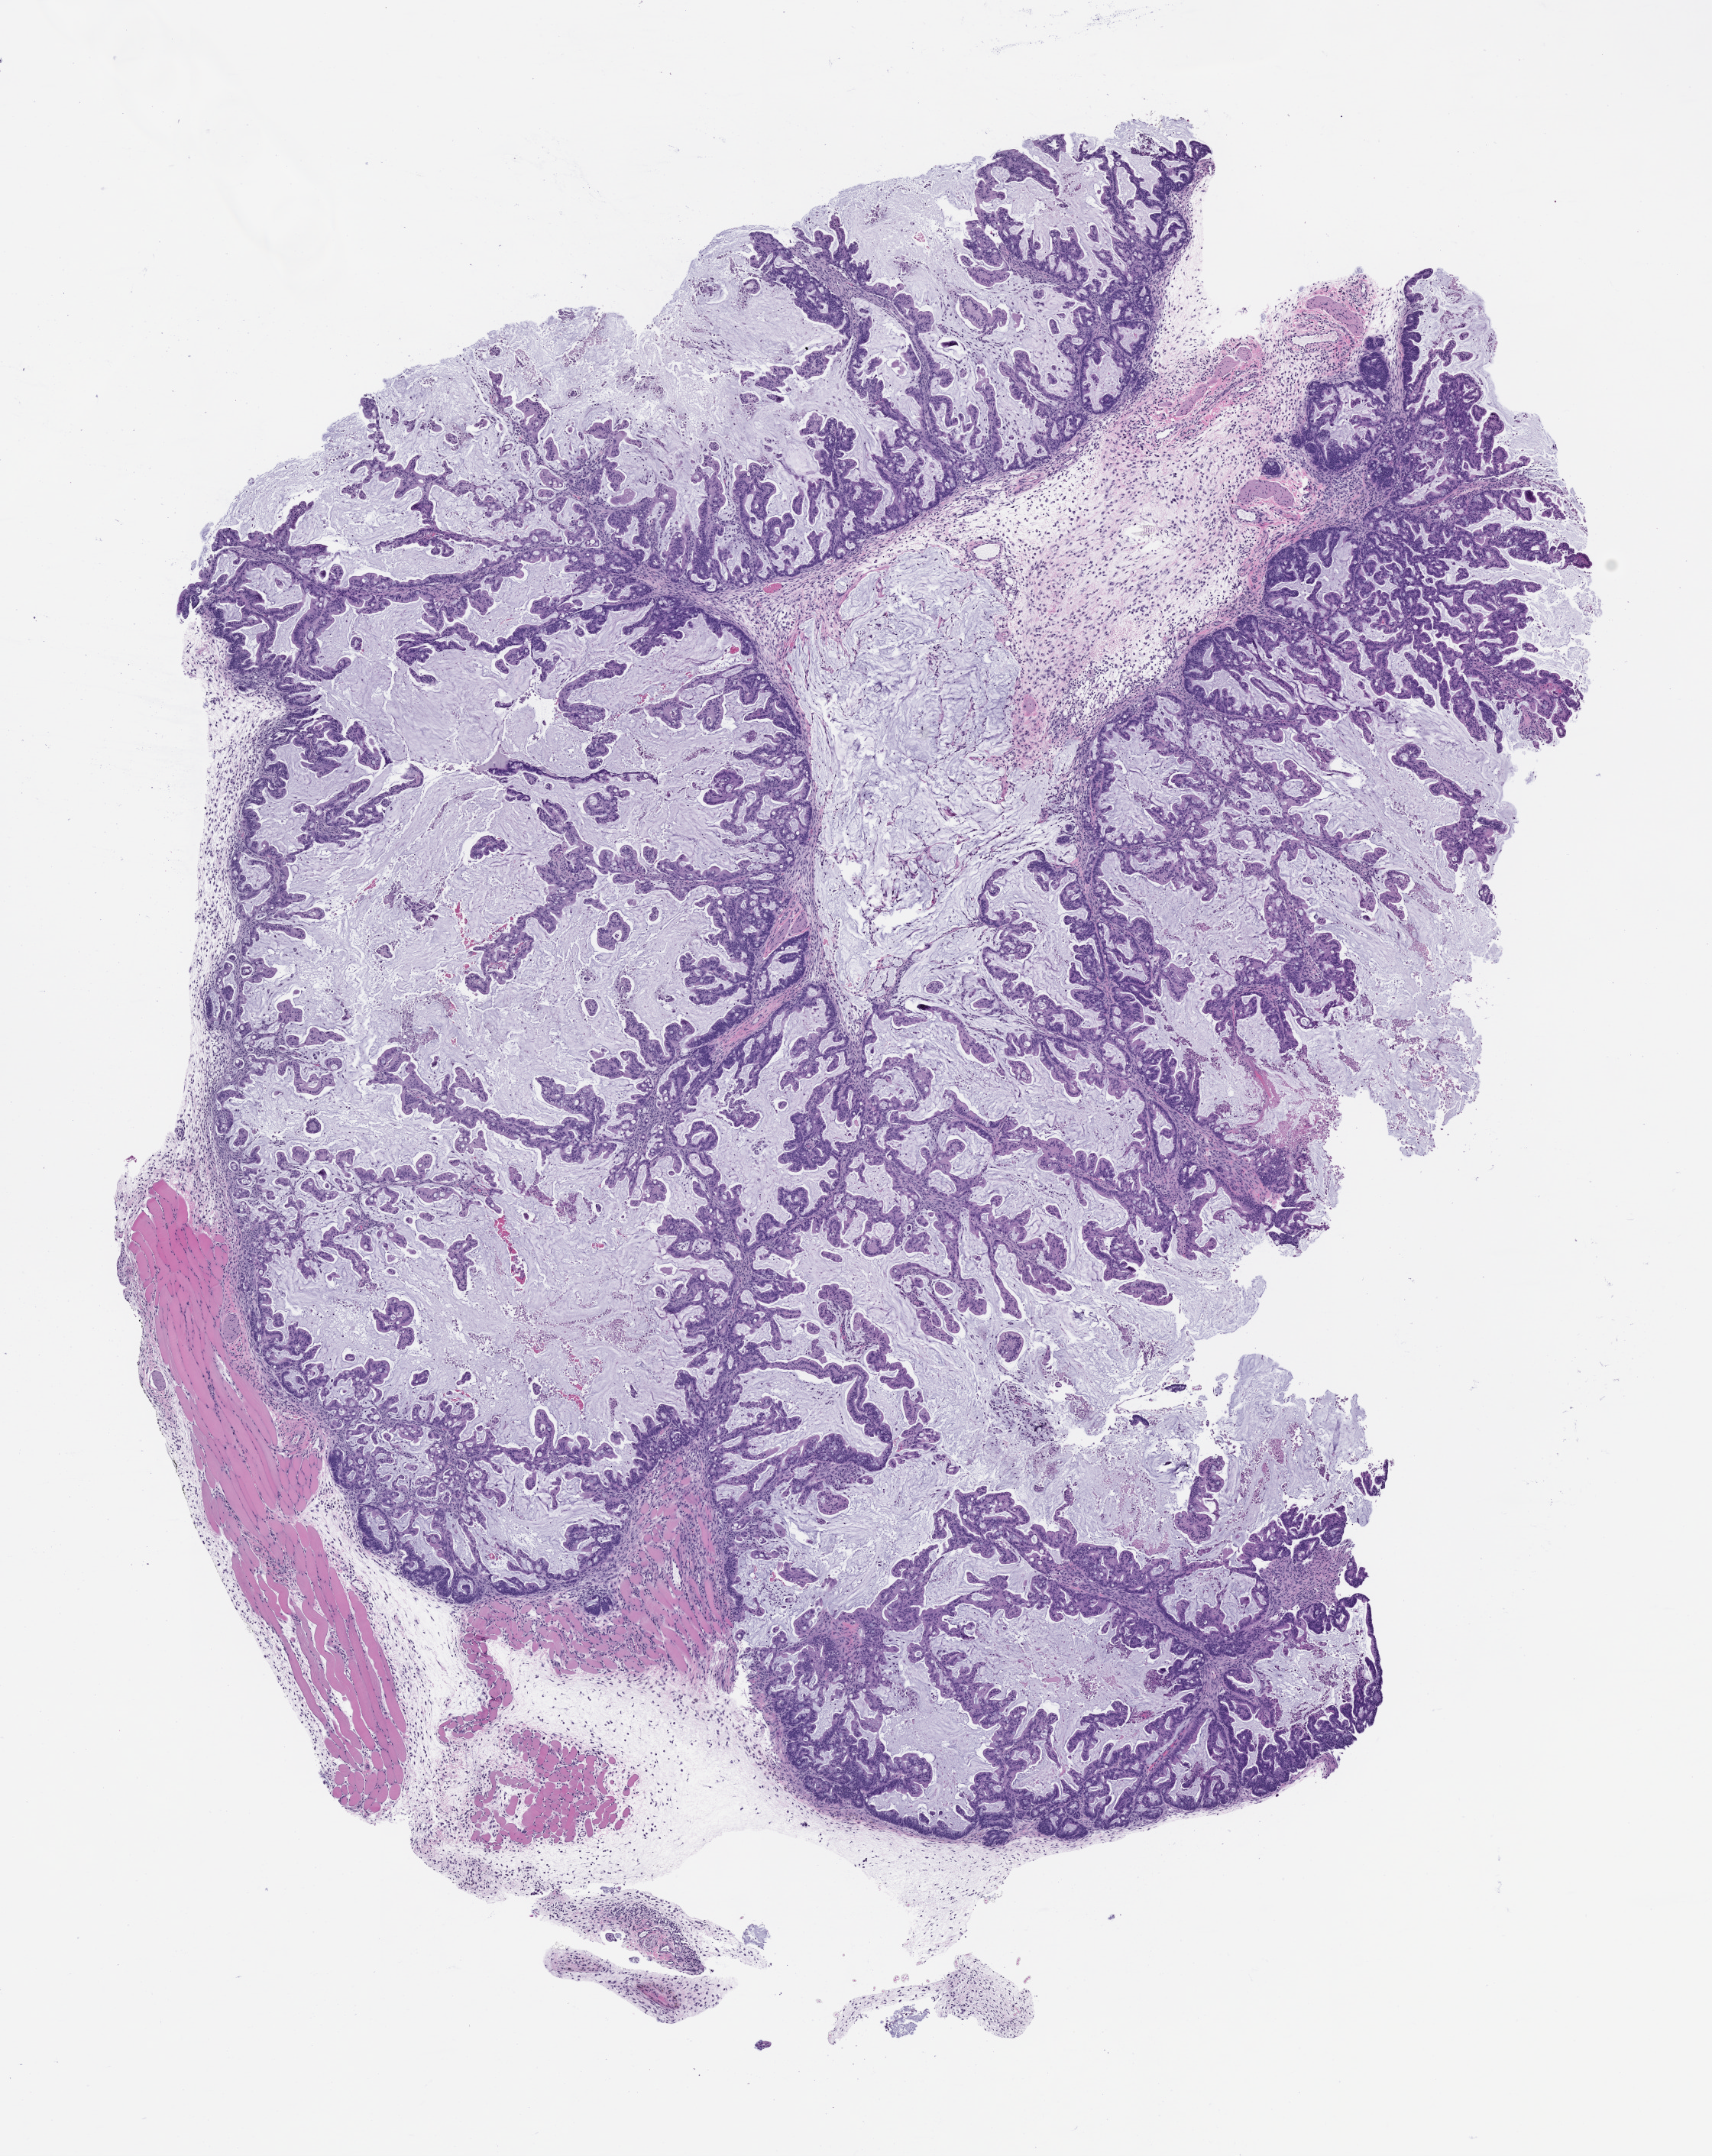
Haematoxylin and eosin whole-slide image of a patient-derived xenograft (PDX) tumor grown in a mouse, passage 0, a low-resolution overview of the entire scanned area, about 9.0 x 11.3 mm. Formalin-fixed paraffin-embedded section. Originating tumor site category: rectum.
Originating patient diagnosis: Rectal Adenocarcinoma.